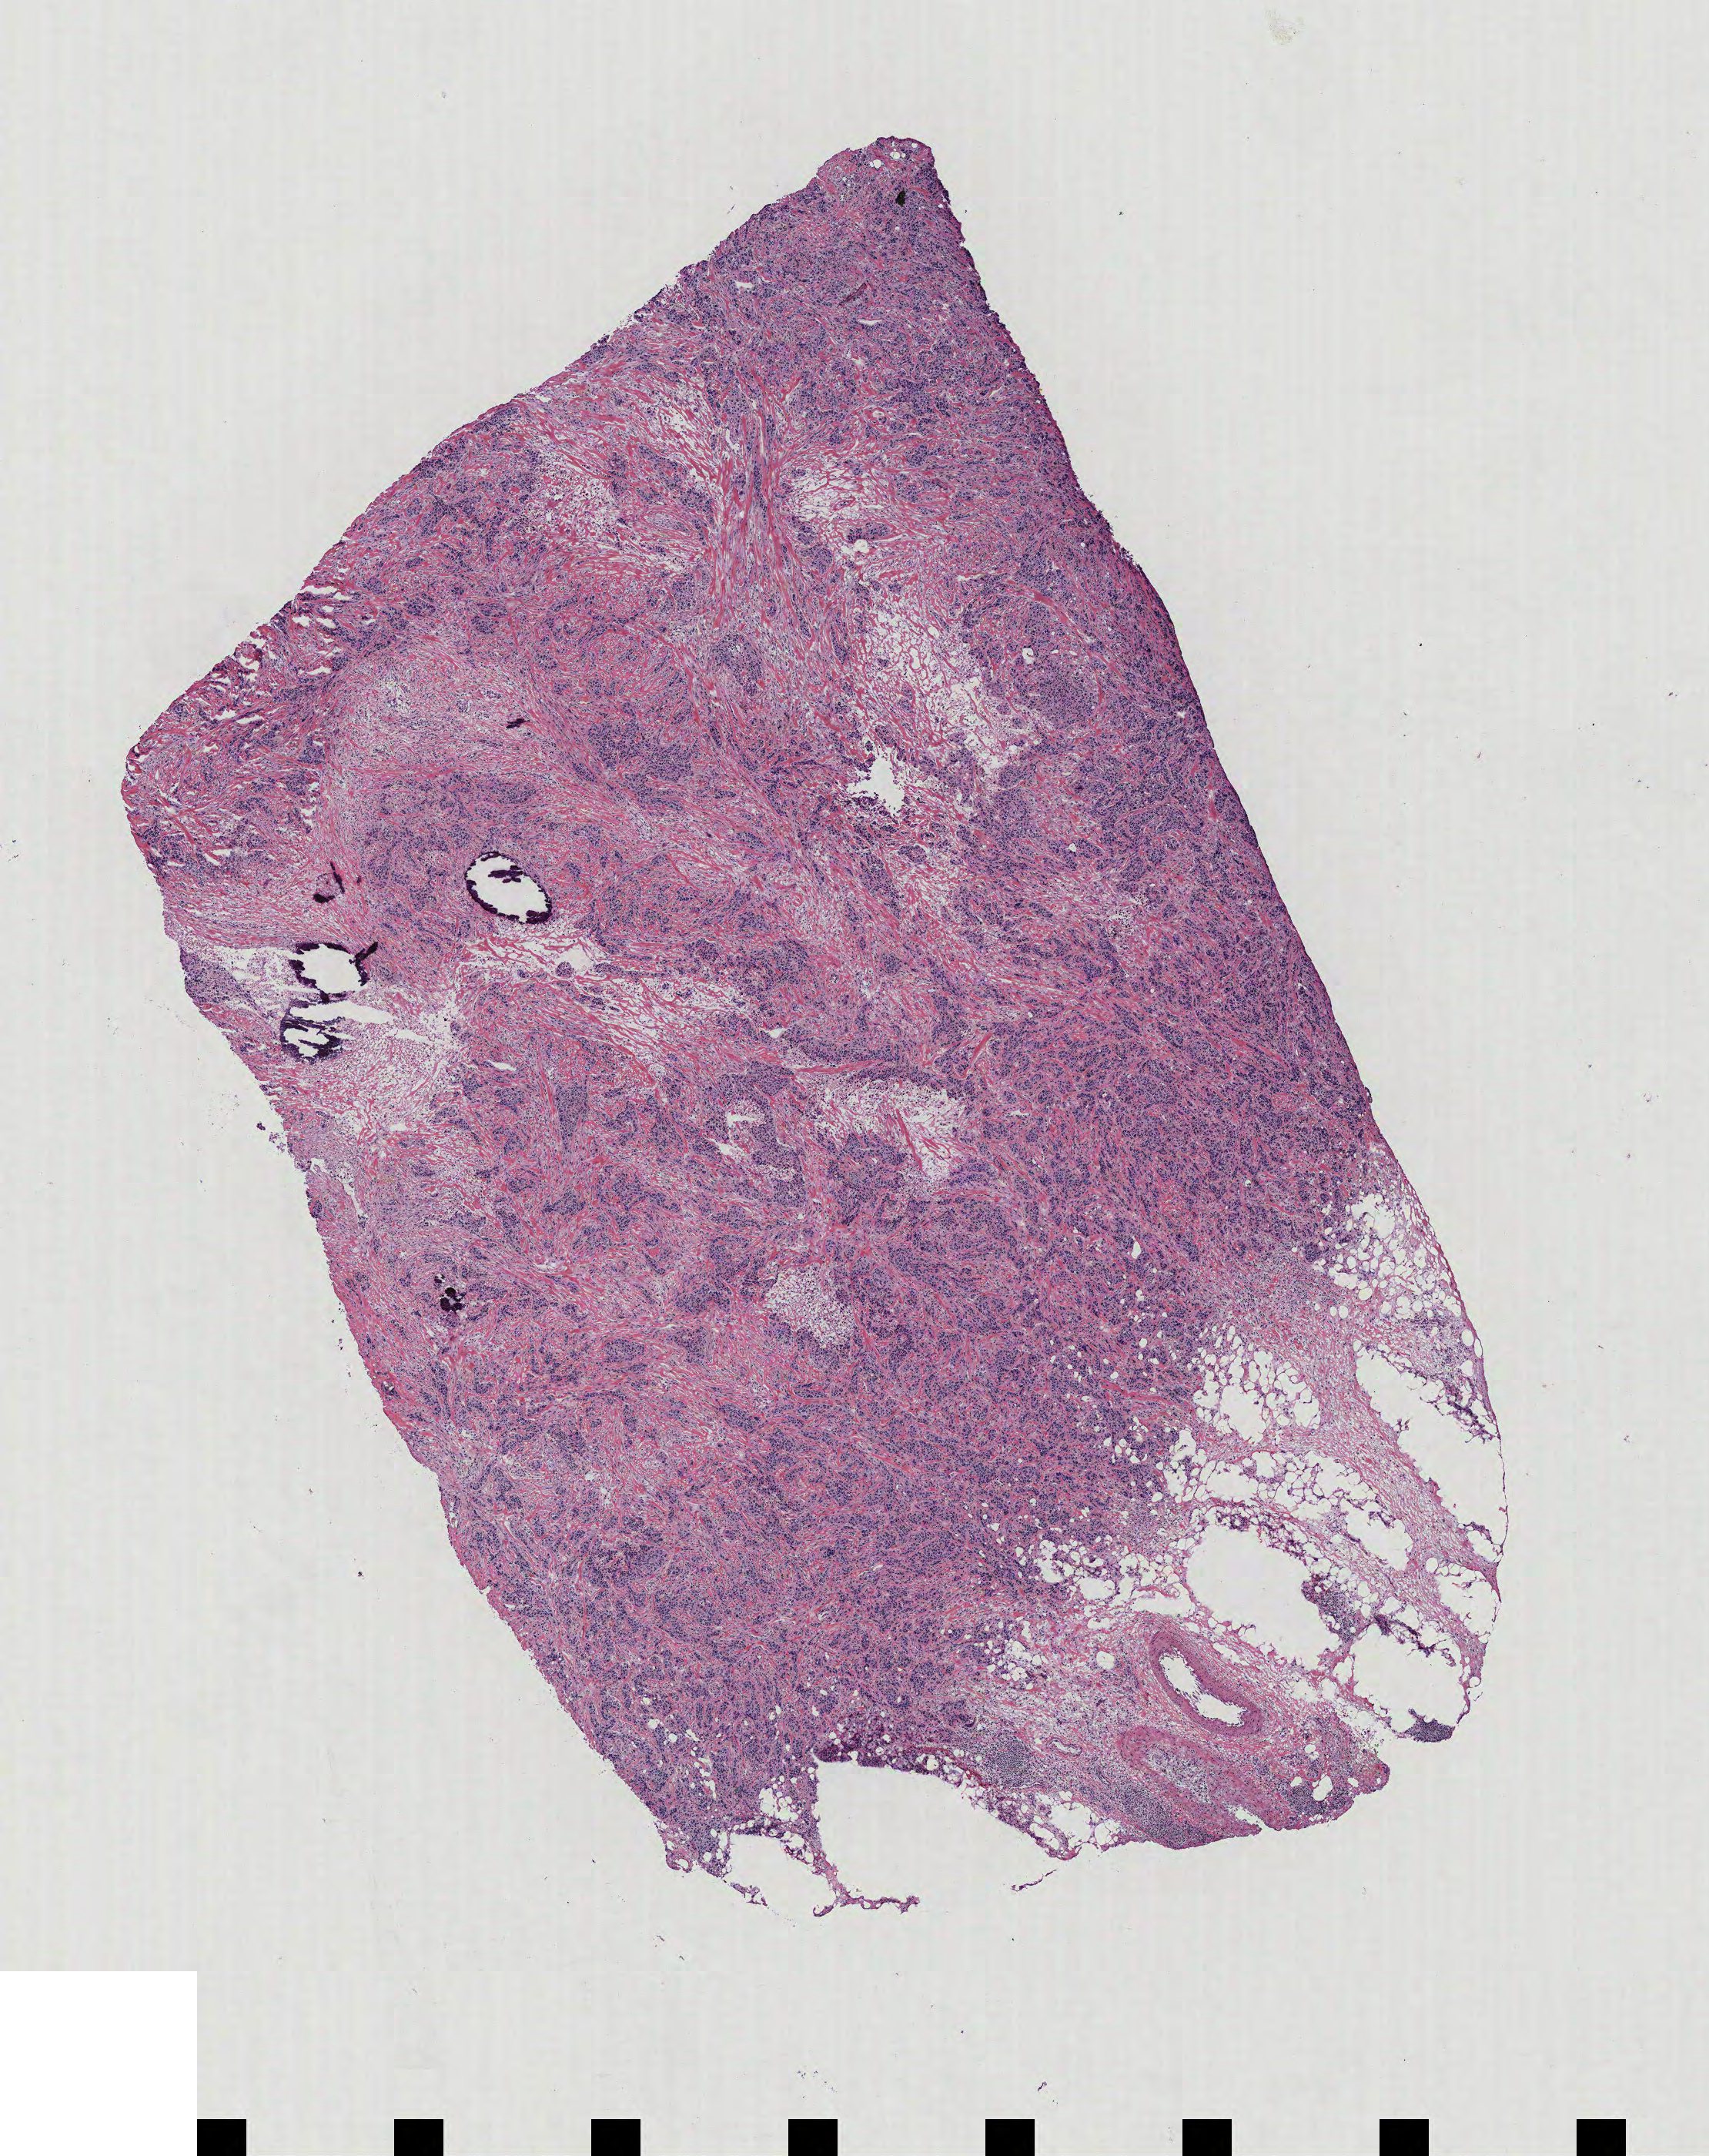
Digitized H&E-stained tissue section (whole slide) — a low-resolution overview of the entire scanned area, about 8.9 x 11.2 mm (from a 40x scan); breast, tumour tissue. Patient: female, age 47 years.
Diagnosis: Infiltrating duct carcinoma, NOS. AJCC pathologic stage: IIB.